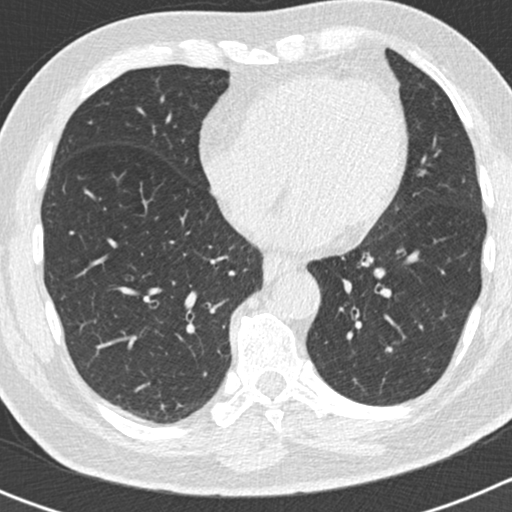
Low-dose screening chest CT, axial slice; second annual screen; lung window (W 1500 / L -600 HU); 2 mm slice thickness; standard (soft-tissue) reconstruction kernel (B30f); slice 106 of 186 in the series. Male participant, aged 66 years at enrolment. Former smoker at enrolment.
Expert-annotated lung lesion, bounding box <343,317,420,401> (left, top, right, bottom; pixels). The exam's reader record, not a measurement of the box and not confirmed to be the same lesion: non-calcified nodule or mass ≥4 mm, left lower lobe, 50 × 33 mm, smooth margins, pre-existing on the prior screen: yes; interval growth: yes. Participant outcome: lung cancer diagnosed 440 days after this screen — adenocarcinoma, NOS, left lower lobe, poorly differentiated (G3), stage IB (AJCC 6th edition), 38 mm at pathology.